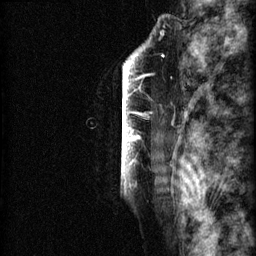
Breast MRI (dynamic contrast-enhanced), one sagittal slice; slice 56 of 60 in the series (ordered by position); 3 images stored at this slice position (order not interpretable as contrast timing); 1.5 T; TE 4.2 ms, TR 22.7 ms; 256 × 256 image matrix, field of view 180 × 180 mm. Patient: female, 48 years. From the clinical record (not read from this slice): setting: breast cancer imaged before/during neoadjuvant chemotherapy; receptor status: triple-negative.
Structures marked on this image (semi-automatic segmentation, software-assisted and operator-edited):
- analysis volume of interest (the breast-tissue region the enhancement analysis was run in; not a lesion): bounding box <86,30,173,207> (left, top, right, bottom; pixels)
- tumour enhancement mask (voxels above the 90 % enhancement threshold inside the analysis volume of interest): <122,44,152,194>